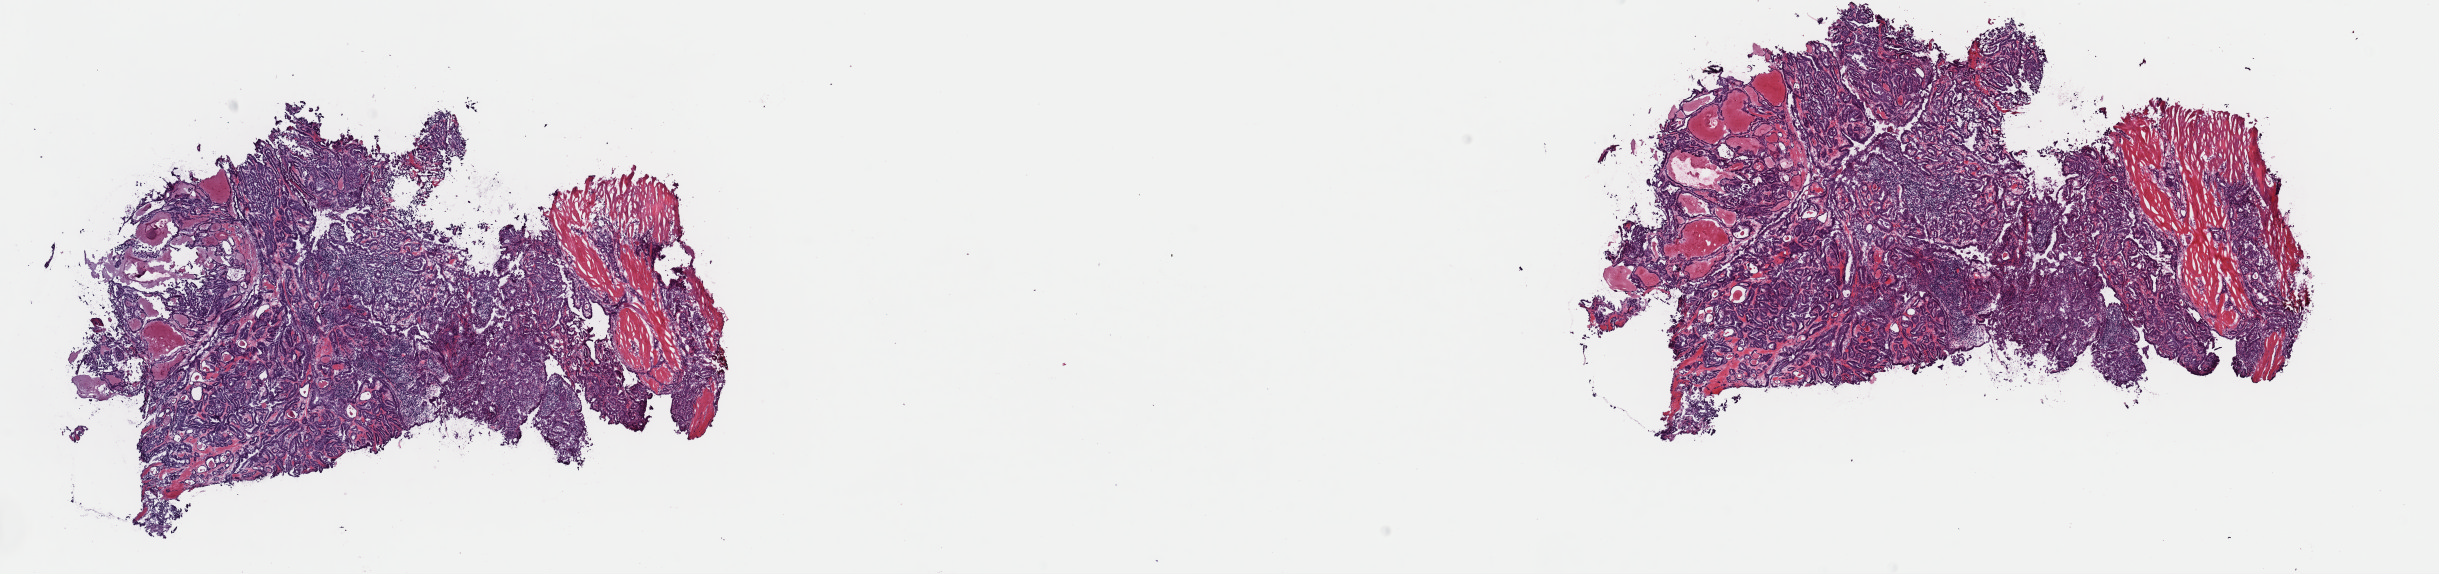
Digitized H&E-stained tissue section (whole slide), whole scanned area (about 19.3 x 4.5 mm) shown as a low-resolution overview, frozen section, sample: primary tumour, thyroid. Female patient; age at initial diagnosis 43 years. Composition of this section per pathologist review: tumour cells 75%, tumour nuclei 75%, normal cells 0%, stromal cells 25%, necrosis 0%. Infiltration values recorded for this section: lymphocyte infiltration 13%, monocyte infiltration 0%, neutrophil infiltration 0%.
* lymph nodes positive (case pathology): 3 of 33 examined
* TNM: T2 N1b MX
* AJCC pathologic stage: I (7th edition)
* histologic diagnosis: Papillary adenocarcinoma, NOS